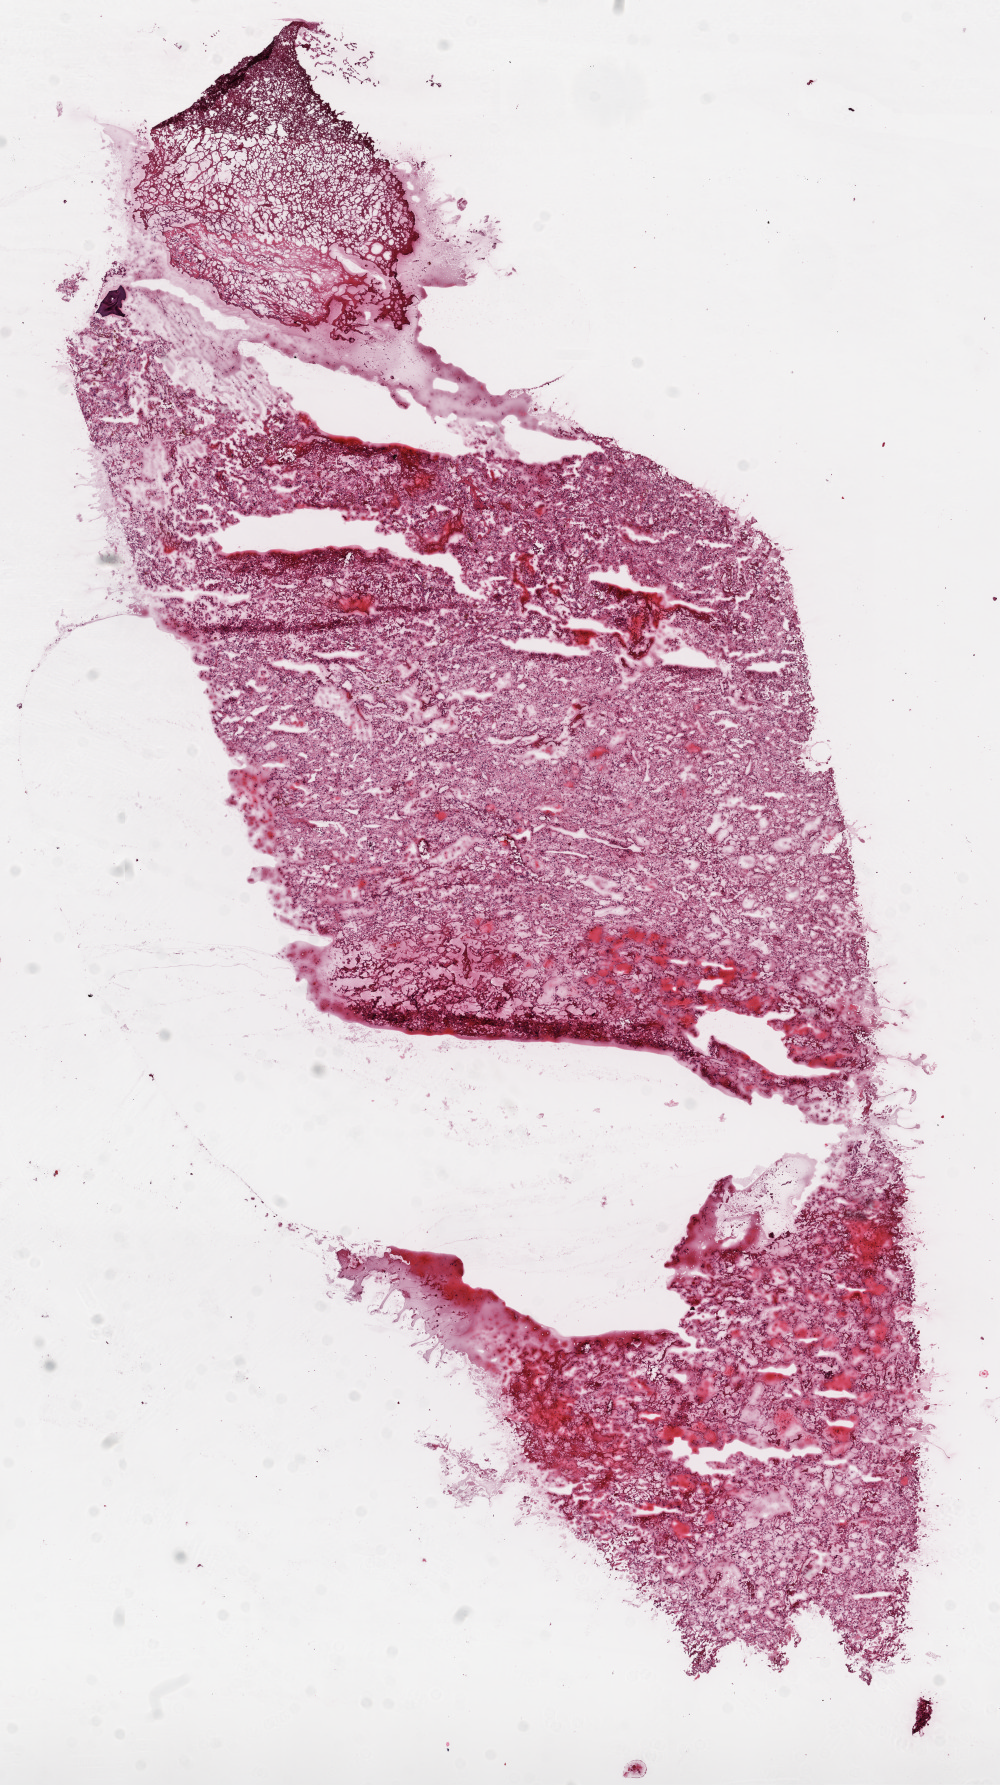
Digitized H&E-stained tissue section (whole slide) — shown as a low-resolution overview of the whole scanned area (about 8.0 x 14.3 mm), frozen section from the top of the tissue portion, primary tumour sample from the kidney. Patient: male, age at initial diagnosis 71 years.
Pathologic diagnosis: Clear cell adenocarcinoma, NOS.